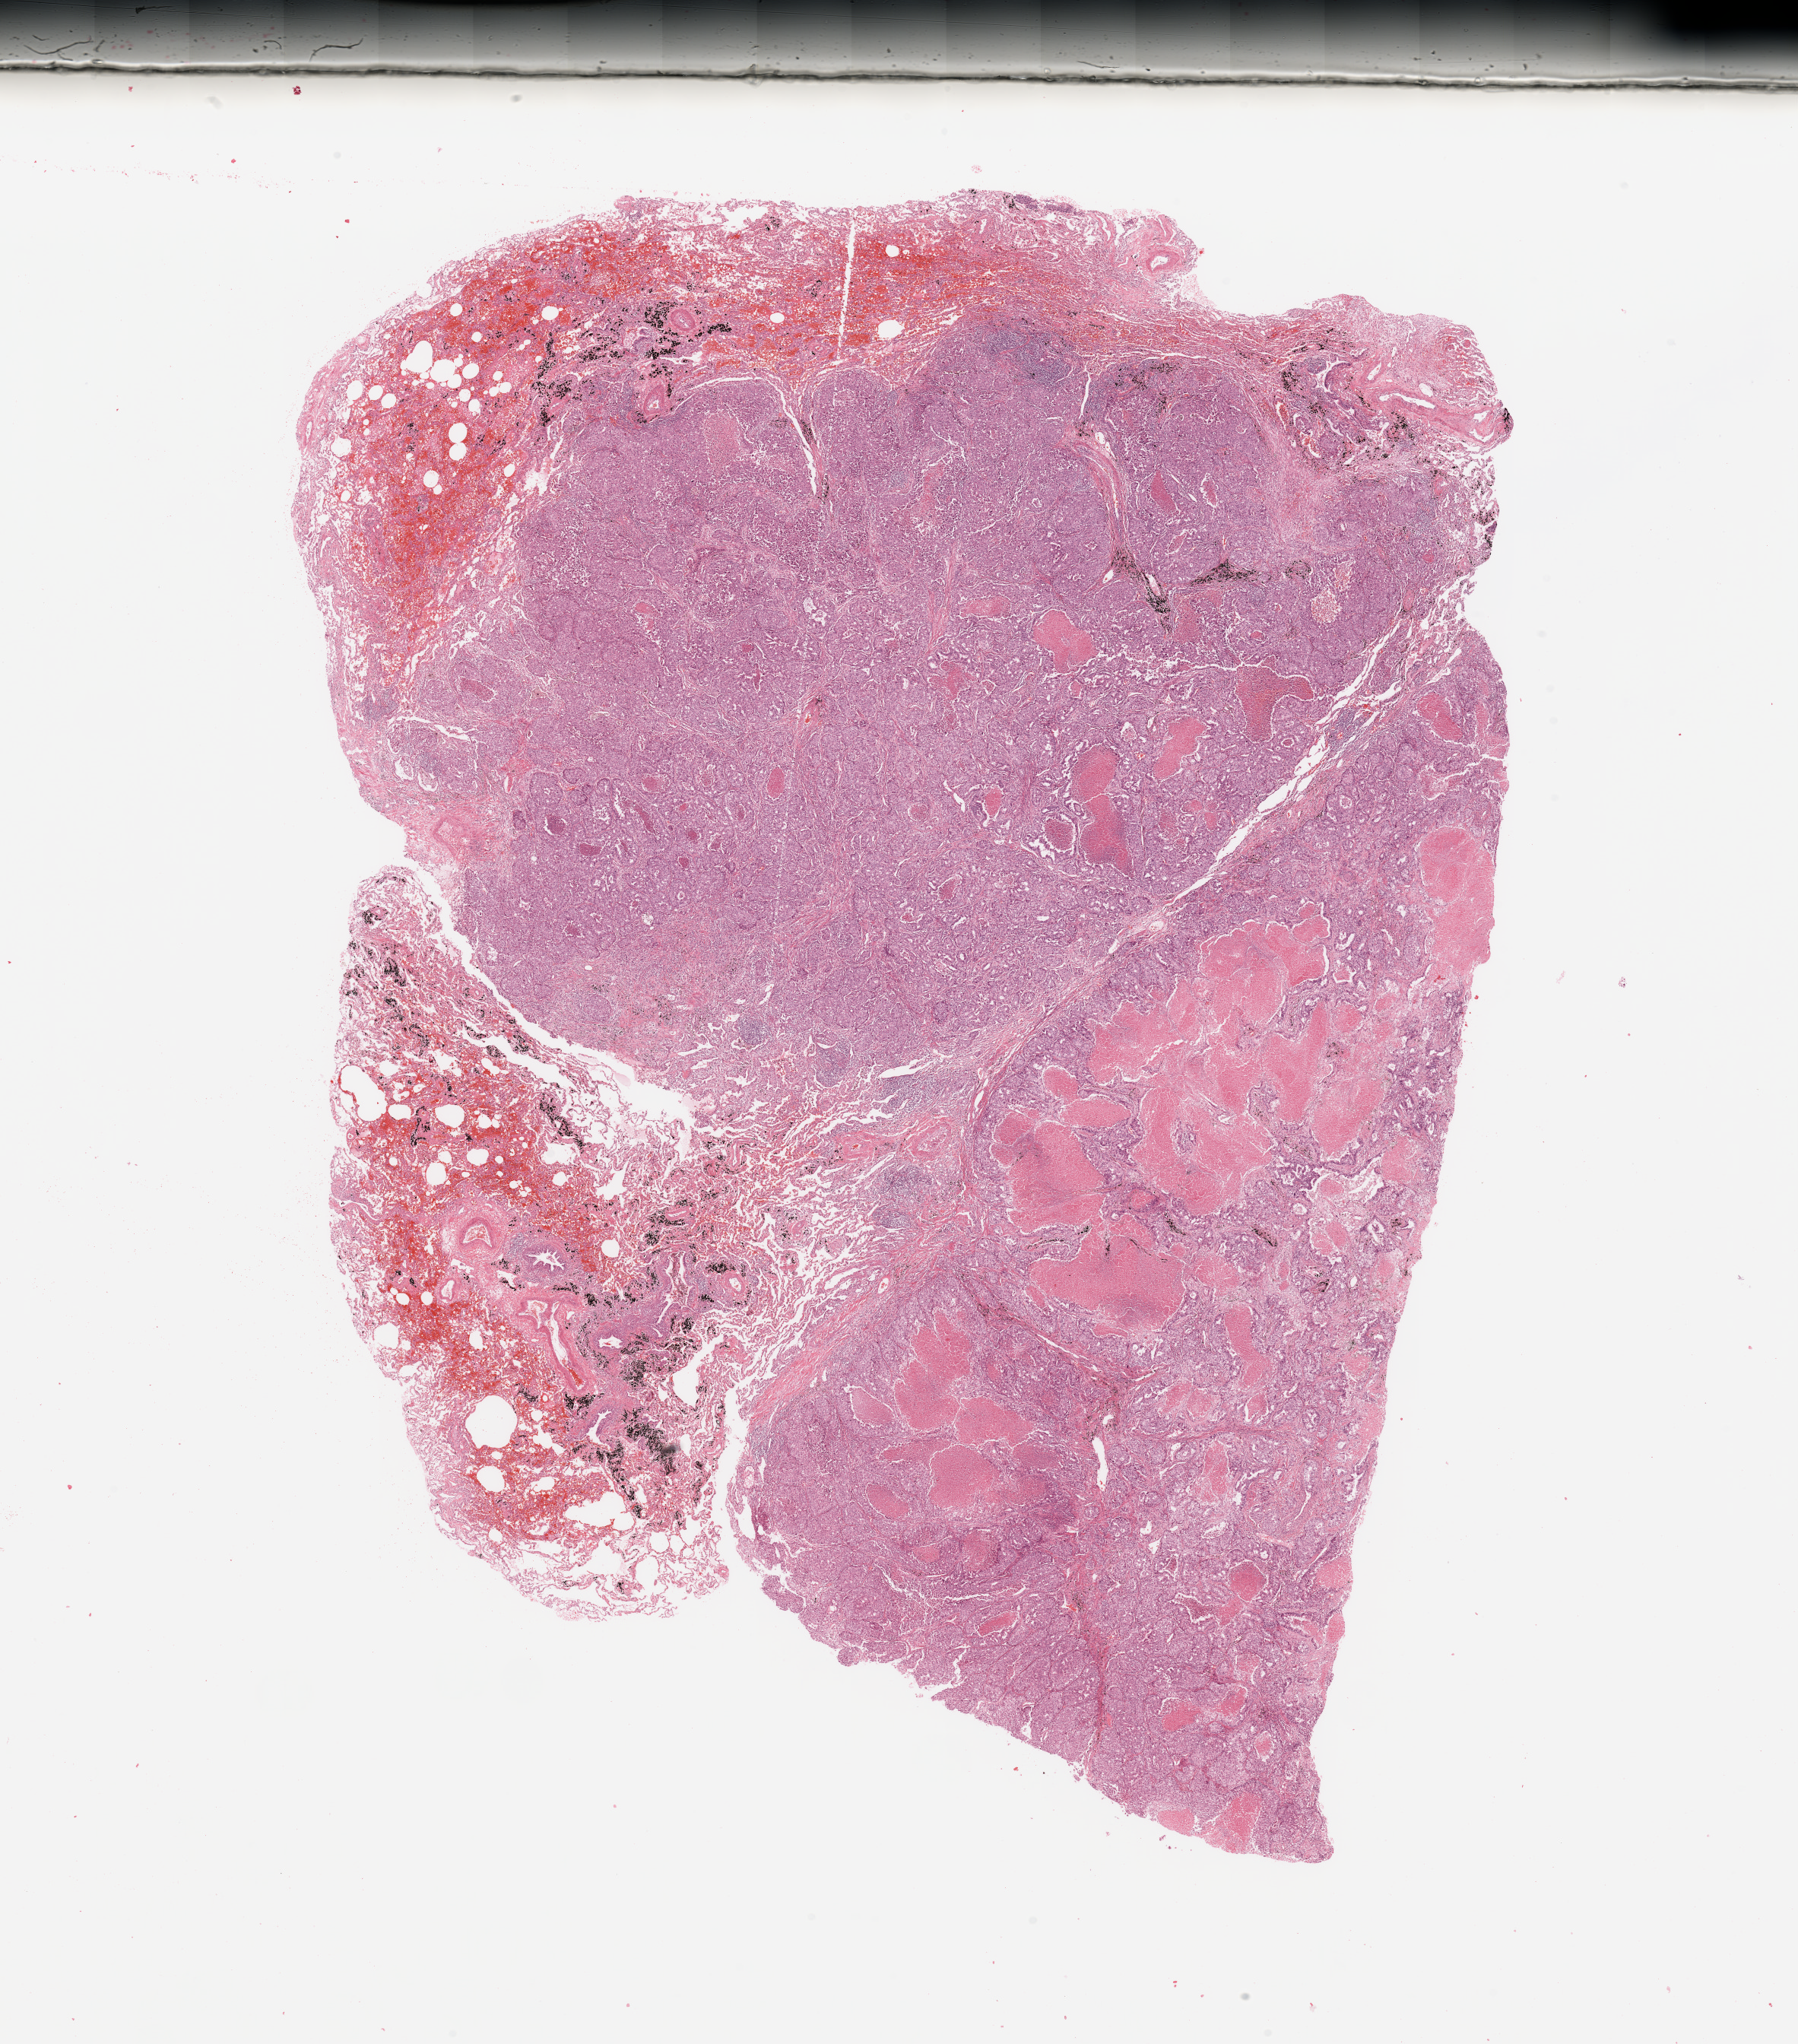
Whole-slide histology image, H&E-stained — a low-resolution overview of the entire scanned area, about 18.7 x 21.3 mm (slide scanned at 20x); lung, tumour tissue. Male, 55 y/o. Histologic grade: G3 (poorly differentiated).
AJCC pathologic stage: IIIA. Histologic diagnosis: Adenocarcinoma, NOS.